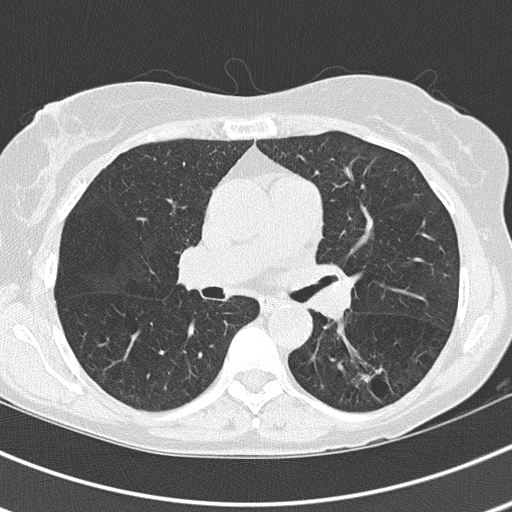
Chest CT (low-dose screening protocol), one axial image; baseline annual screen; lung window (W 1500 / L -600 HU); 120 kVp; slice 66 of 143 in the series. Female, age 60 years at enrolment.
- Expert-annotated lung lesion, bounding box (x1, y1, x2, y2) in pixels: (351, 360, 381, 395).
- Screening reader's record for this exam: no non-calcified nodule ≥4 mm recorded.
- Lung cancer was diagnosed 403 days after this screen: adenocarcinoma, NOS, left lower lobe, well differentiated (G1), stage IA (AJCC 6th edition), 15 mm at pathology.